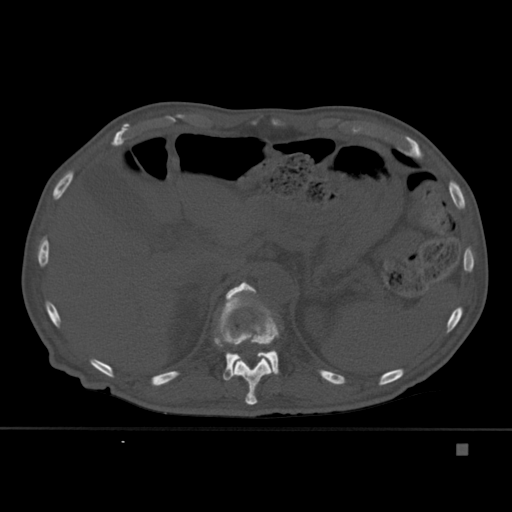
CT including the spine, one axial slice; position 210 of 451 along the scan axis; bone window (W 1800 / L 400 HU); 1.5 mm slice thickness; 512 × 512 image matrix, field of view 378 × 378 mm. Male patient, age 75 years. From the clinical record (not read from this slice): primary cancer: prostate.
Structures marked on this image (semi-automatic segmentation, software-assisted and operator-edited):
- T11 vertebra: box from (x=233, y=300) to (x=280, y=405) px
- T12 vertebra: (x=214, y=281)–(x=281, y=381)